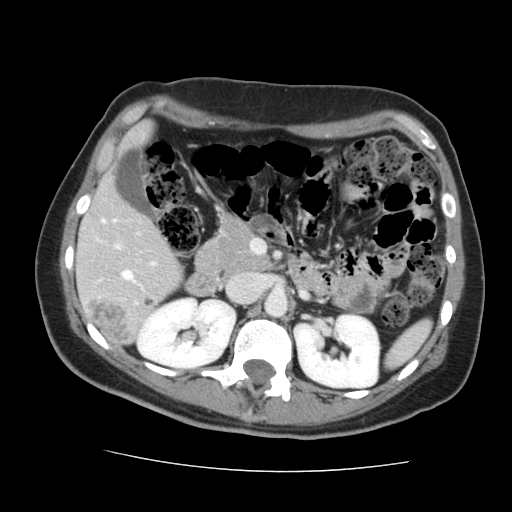
Contrast-enhanced abdominal CT, one axial slice; position 77 of 144 along the scan axis; 120 kVp; intravenous contrast given; soft-tissue window (W 400 / L 40 HU); 2.5 mm slice thickness; 512 × 512 image matrix. Female patient, age 46 years. From the clinical record (not read from this slice): diagnosis: colorectal cancer liver metastases, imaged before liver resection.
Outlined on this slice (expert manual segmentation):
- liver: bounding box [x1, y1, x2, y2] px = [78, 182, 182, 344]
- planned liver remnant (the part of the liver to remain after resection): [78, 182, 182, 337]
- portal vein (with intrahepatic branches): [102, 220, 154, 283]
- liver metastasis: [146, 300, 154, 307]
- liver metastasis: [89, 299, 129, 342]